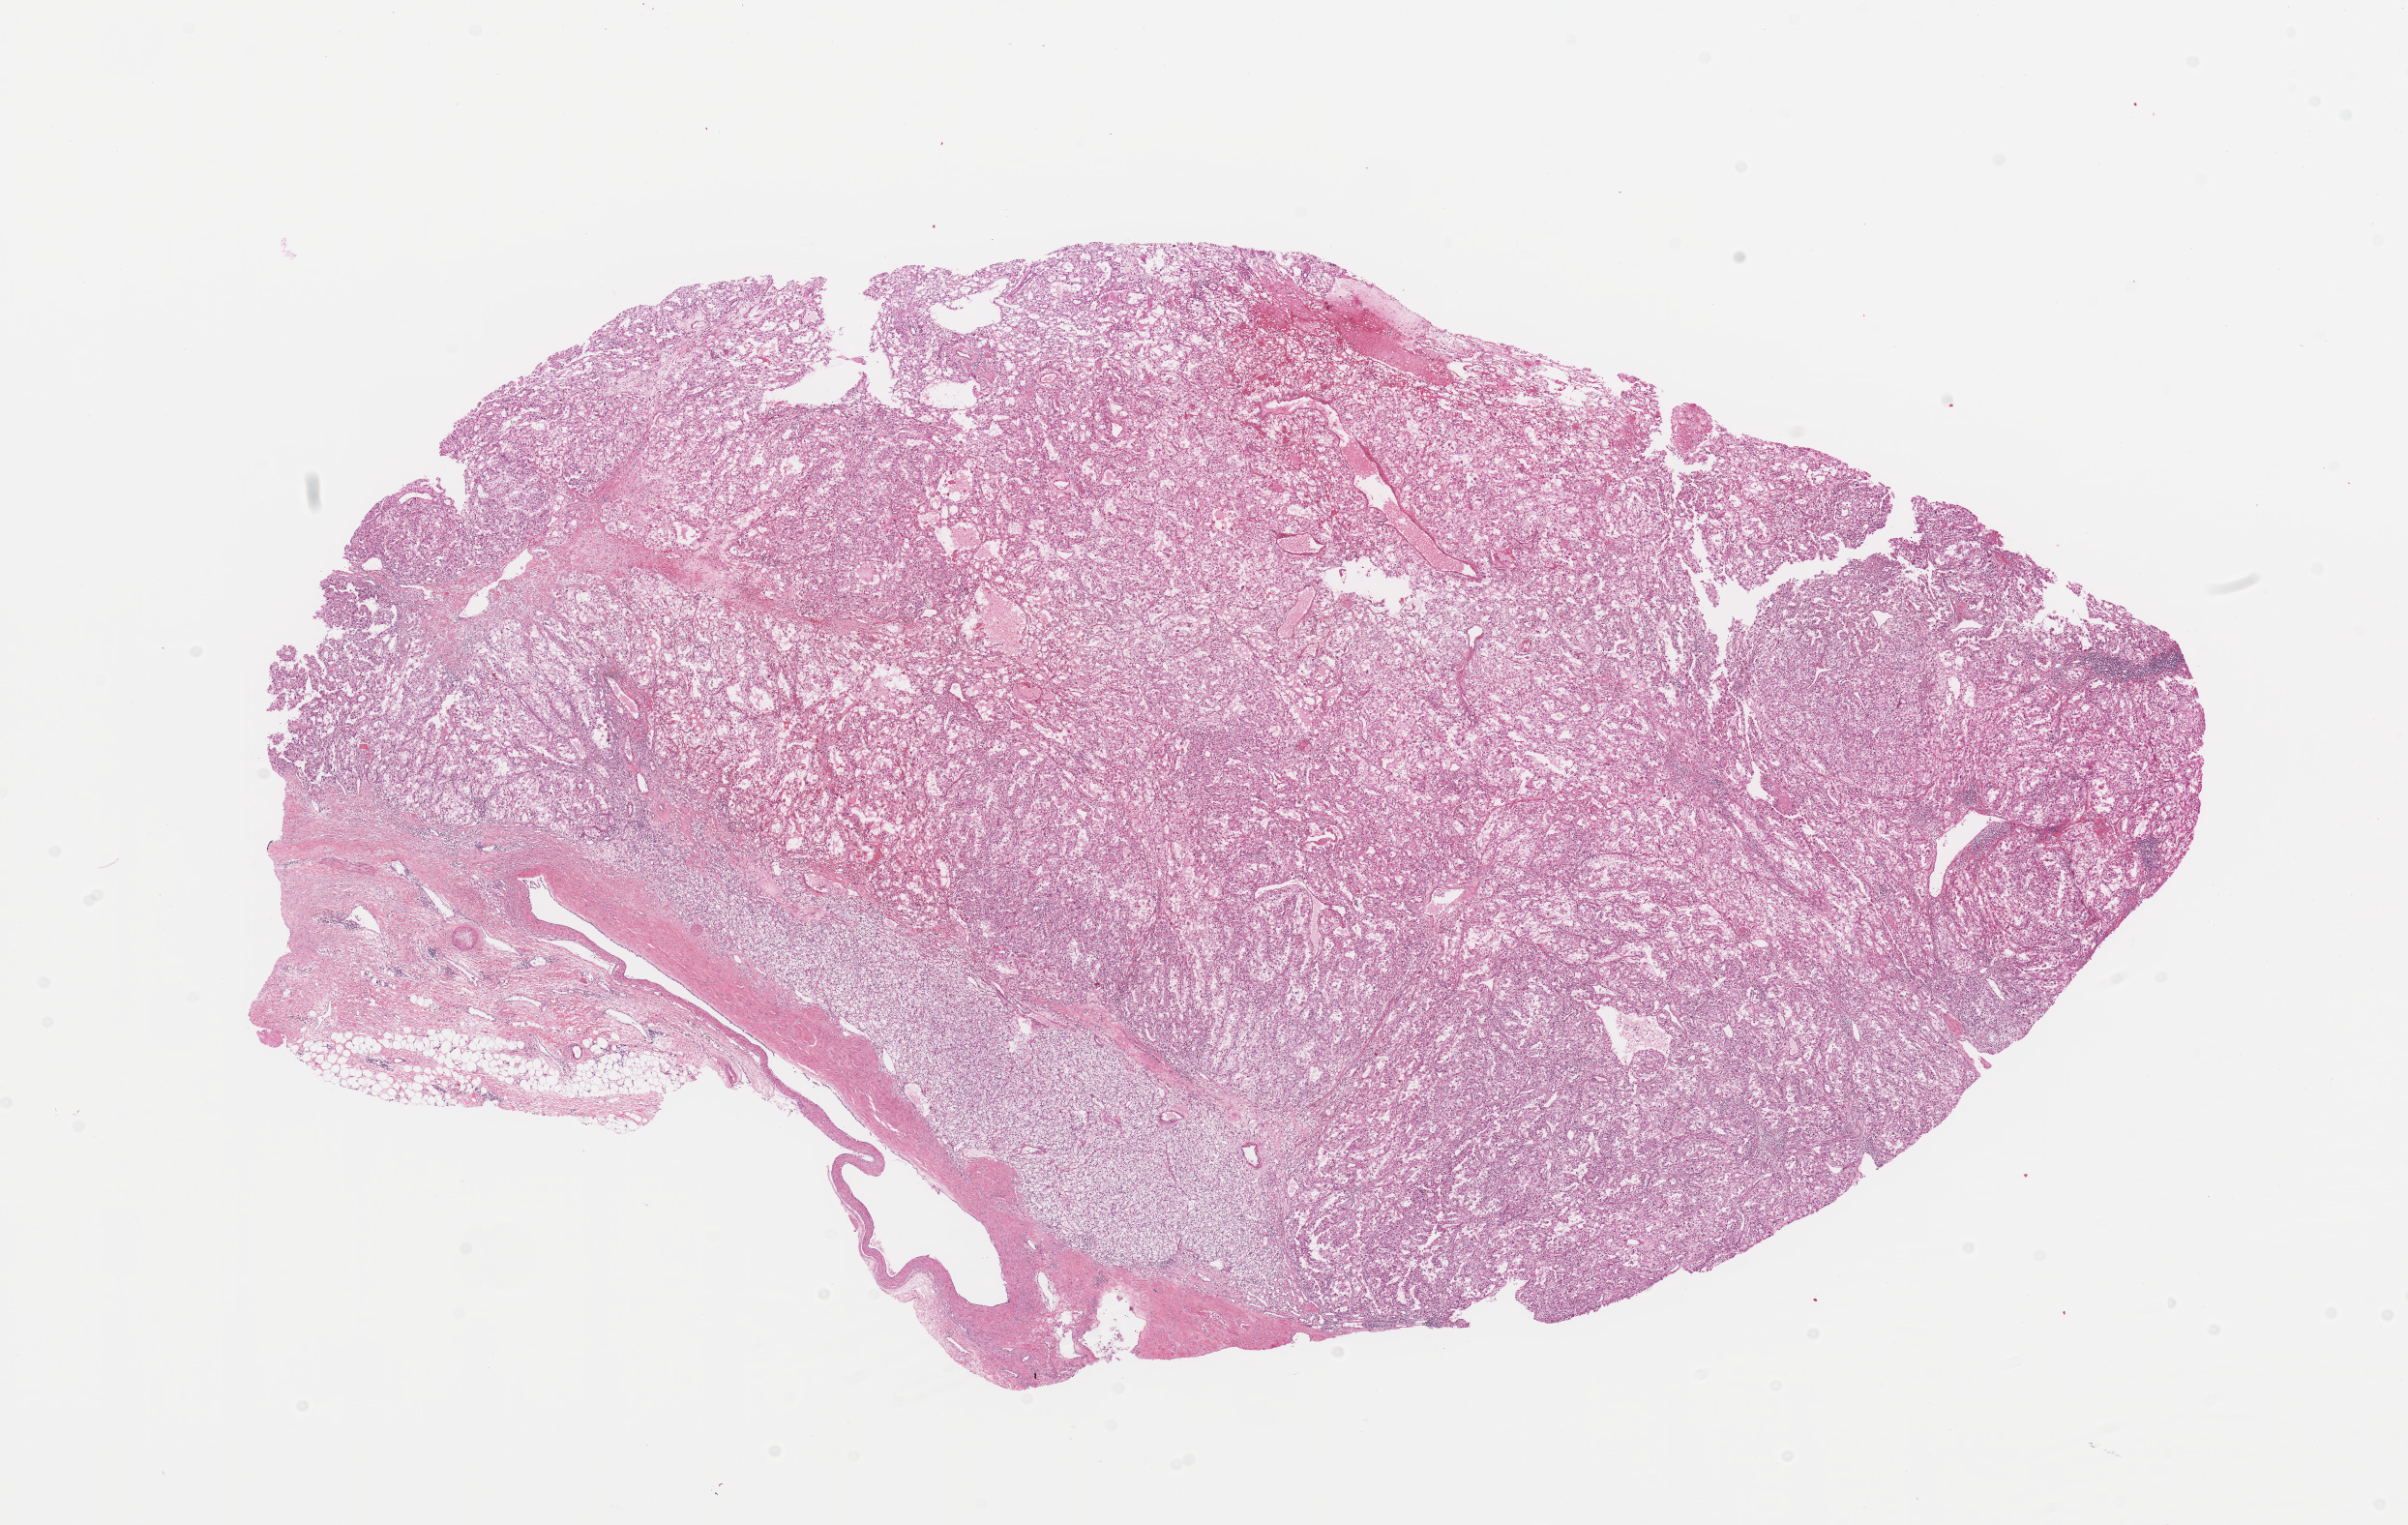
Digitized H&E tissue section (whole slide) — a low-resolution overview of the entire scanned area, about 19.7 x 12.5 mm (slide scanned at 20x). Kidney, tumour tissue. Patient: male, age 67 years. Histologic grade: G2 (moderately differentiated).
• primary tumour site (as recorded): upper pole
• AJCC pathologic stage: I
• histologic diagnosis: Renal cell carcinoma, NOS